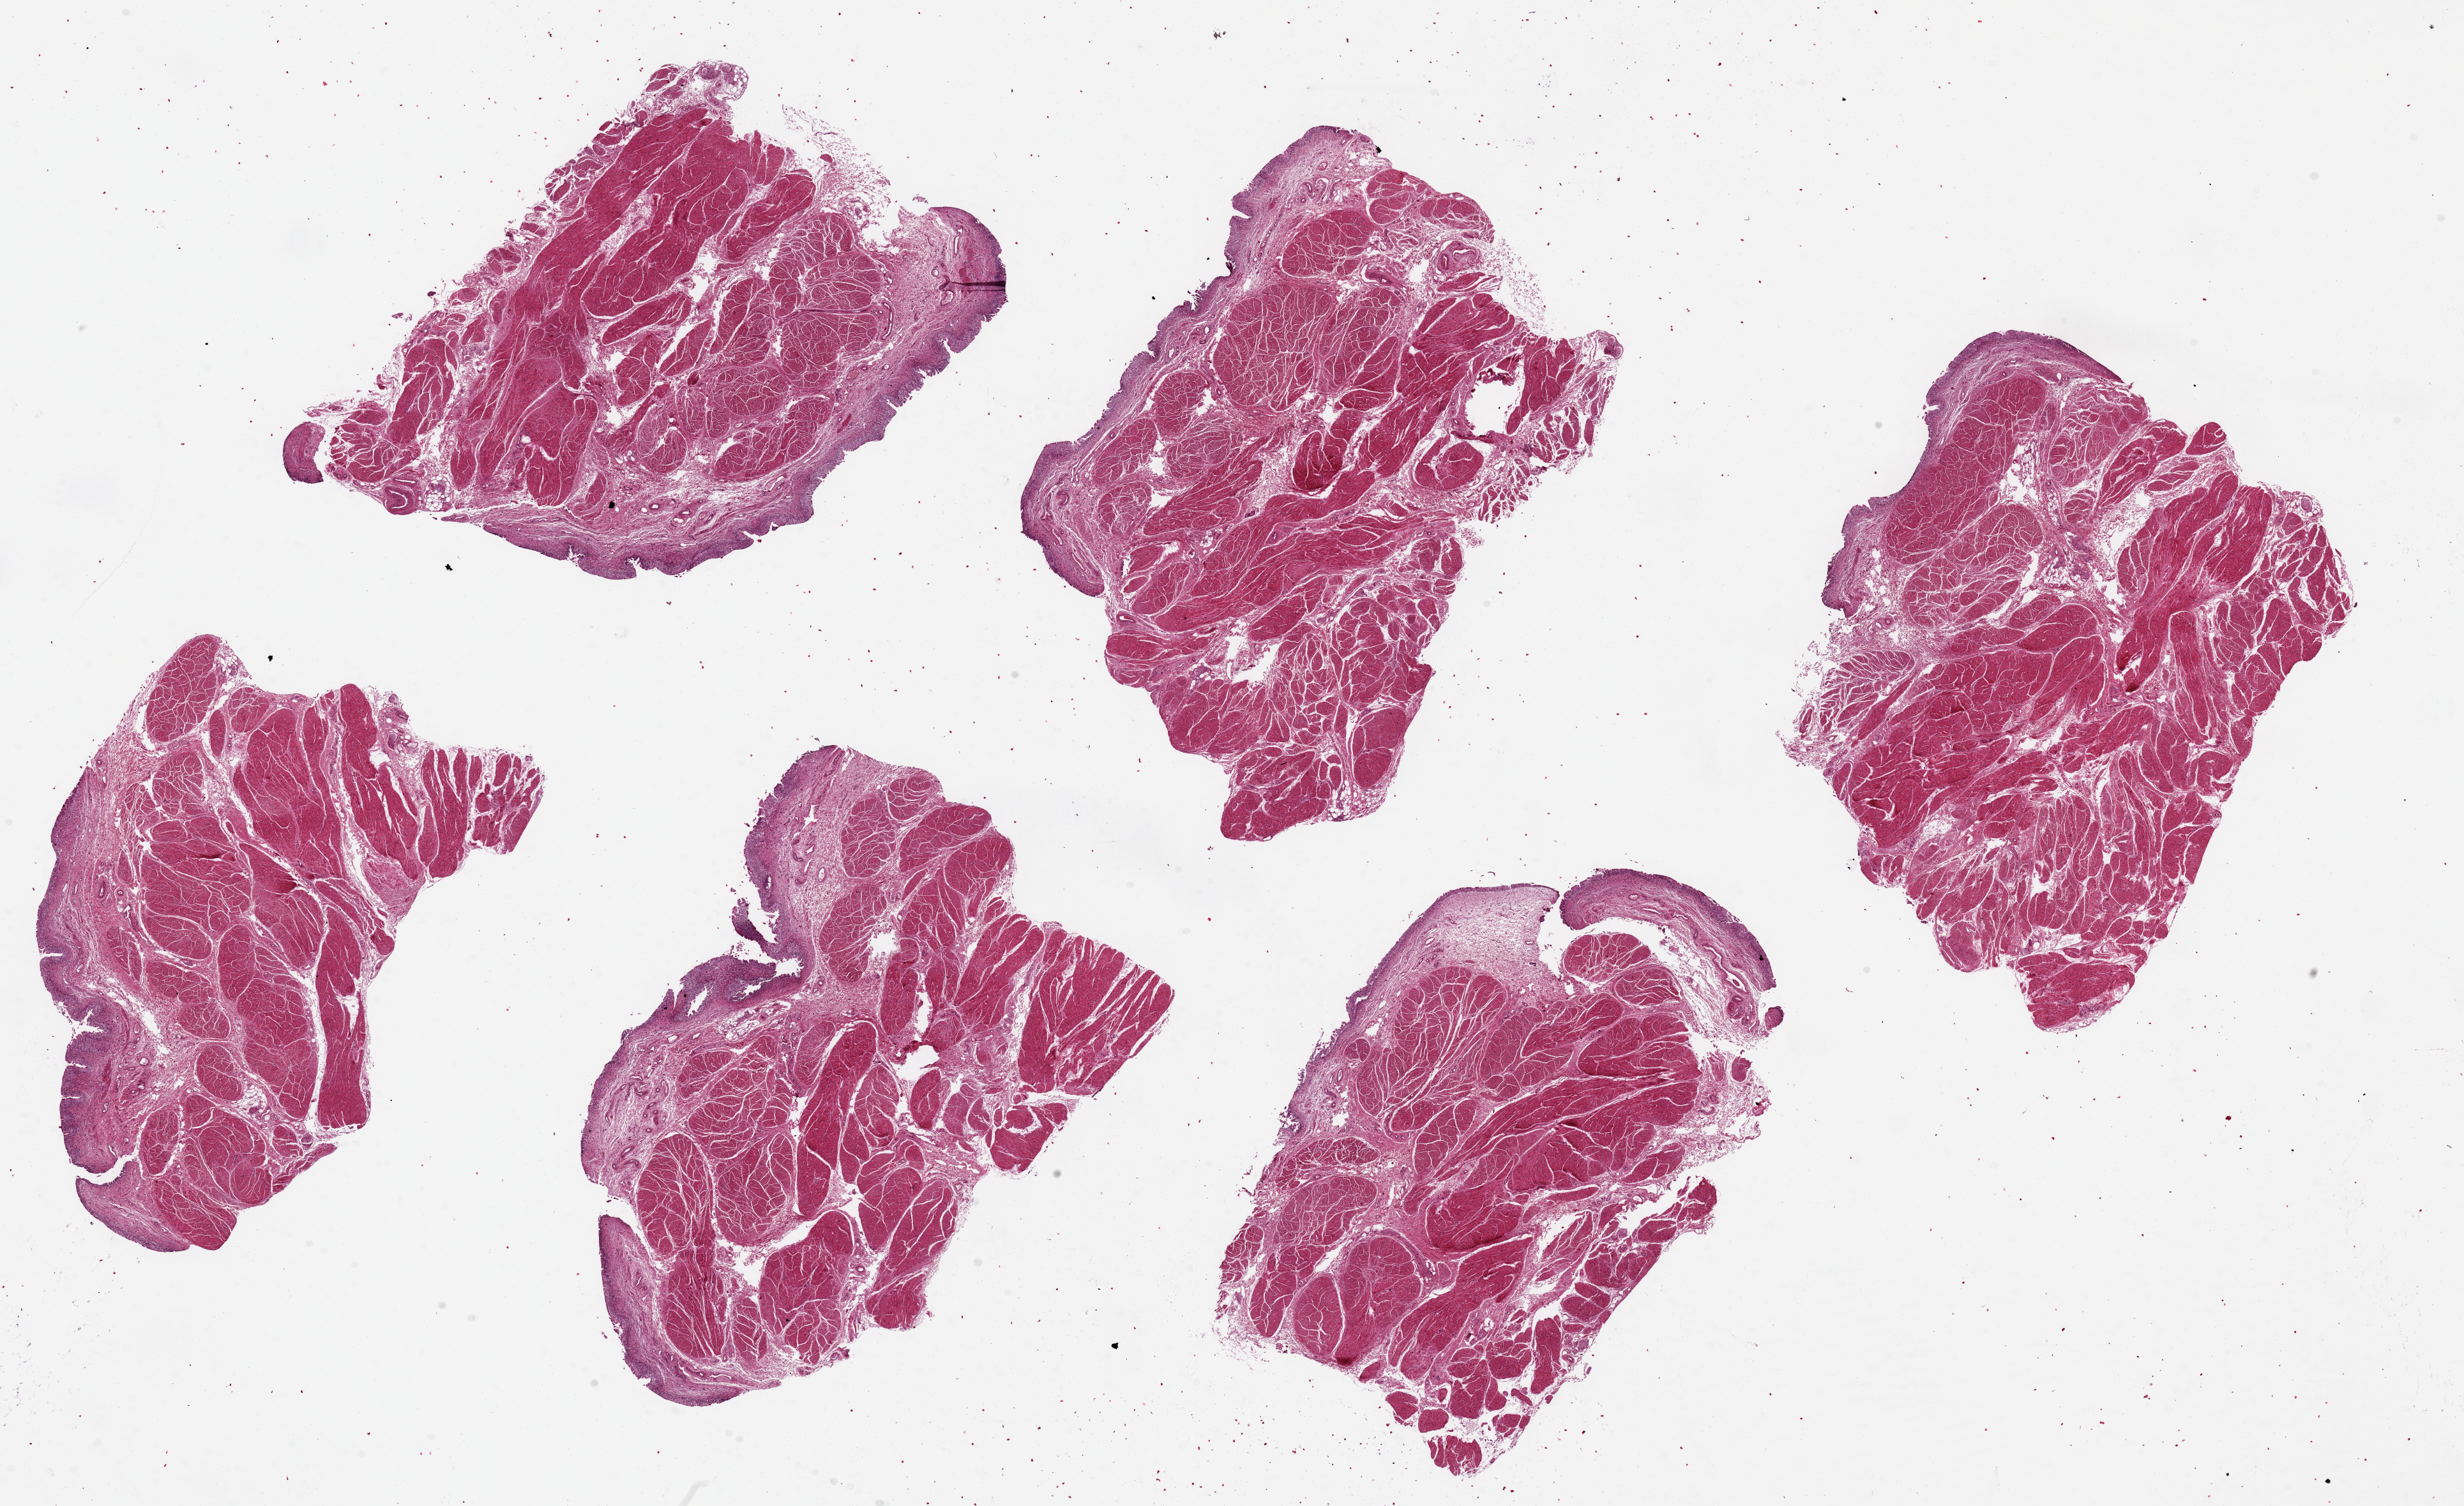
Digitized H&E-stained section, a low-resolution overview of the entire scanned area, about 30.5 x 18.7 mm (slide scanned at 20x). PAXgene-fixed paraffin-embedded (PFPE) section. Sampled site (target tissue): urinary bladder. Tissue donor sample. Female donor.
Pathologist's review note for this sample: 6 pieces ~7x5mm. Urothelium partly sloughed but better preserved than usual.